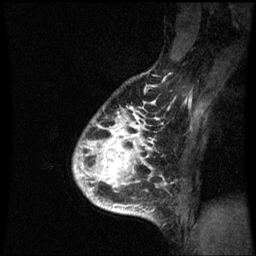
Breast MRI (dynamic contrast-enhanced), one sagittal slice; slice 51 of 60 in the series (ordered by position); dynamic contrast-enhanced series, image 2 of 3 at this slice position (ordered by acquisition); 1.5 T; TE 4.2 ms, TR 8.9 ms; 2 mm slice thickness; 256 × 256 image matrix, field of view 200 × 200 mm. Patient: female, 35 years. Case-level facts recorded for this patient, not image findings: setting: breast cancer imaged before/during neoadjuvant chemotherapy; receptor status: HR-positive, HER2-negative.
Structures marked on this image (semi-automatic segmentation, software-assisted and operator-edited):
- analysis volume of interest (the breast-tissue region the enhancement analysis was run in; not a lesion): box from (x=75, y=100) to (x=165, y=215) px
- tumour enhancement mask (voxels above the 70 % enhancement threshold inside the analysis volume of interest): (x=75, y=102)–(x=155, y=215)